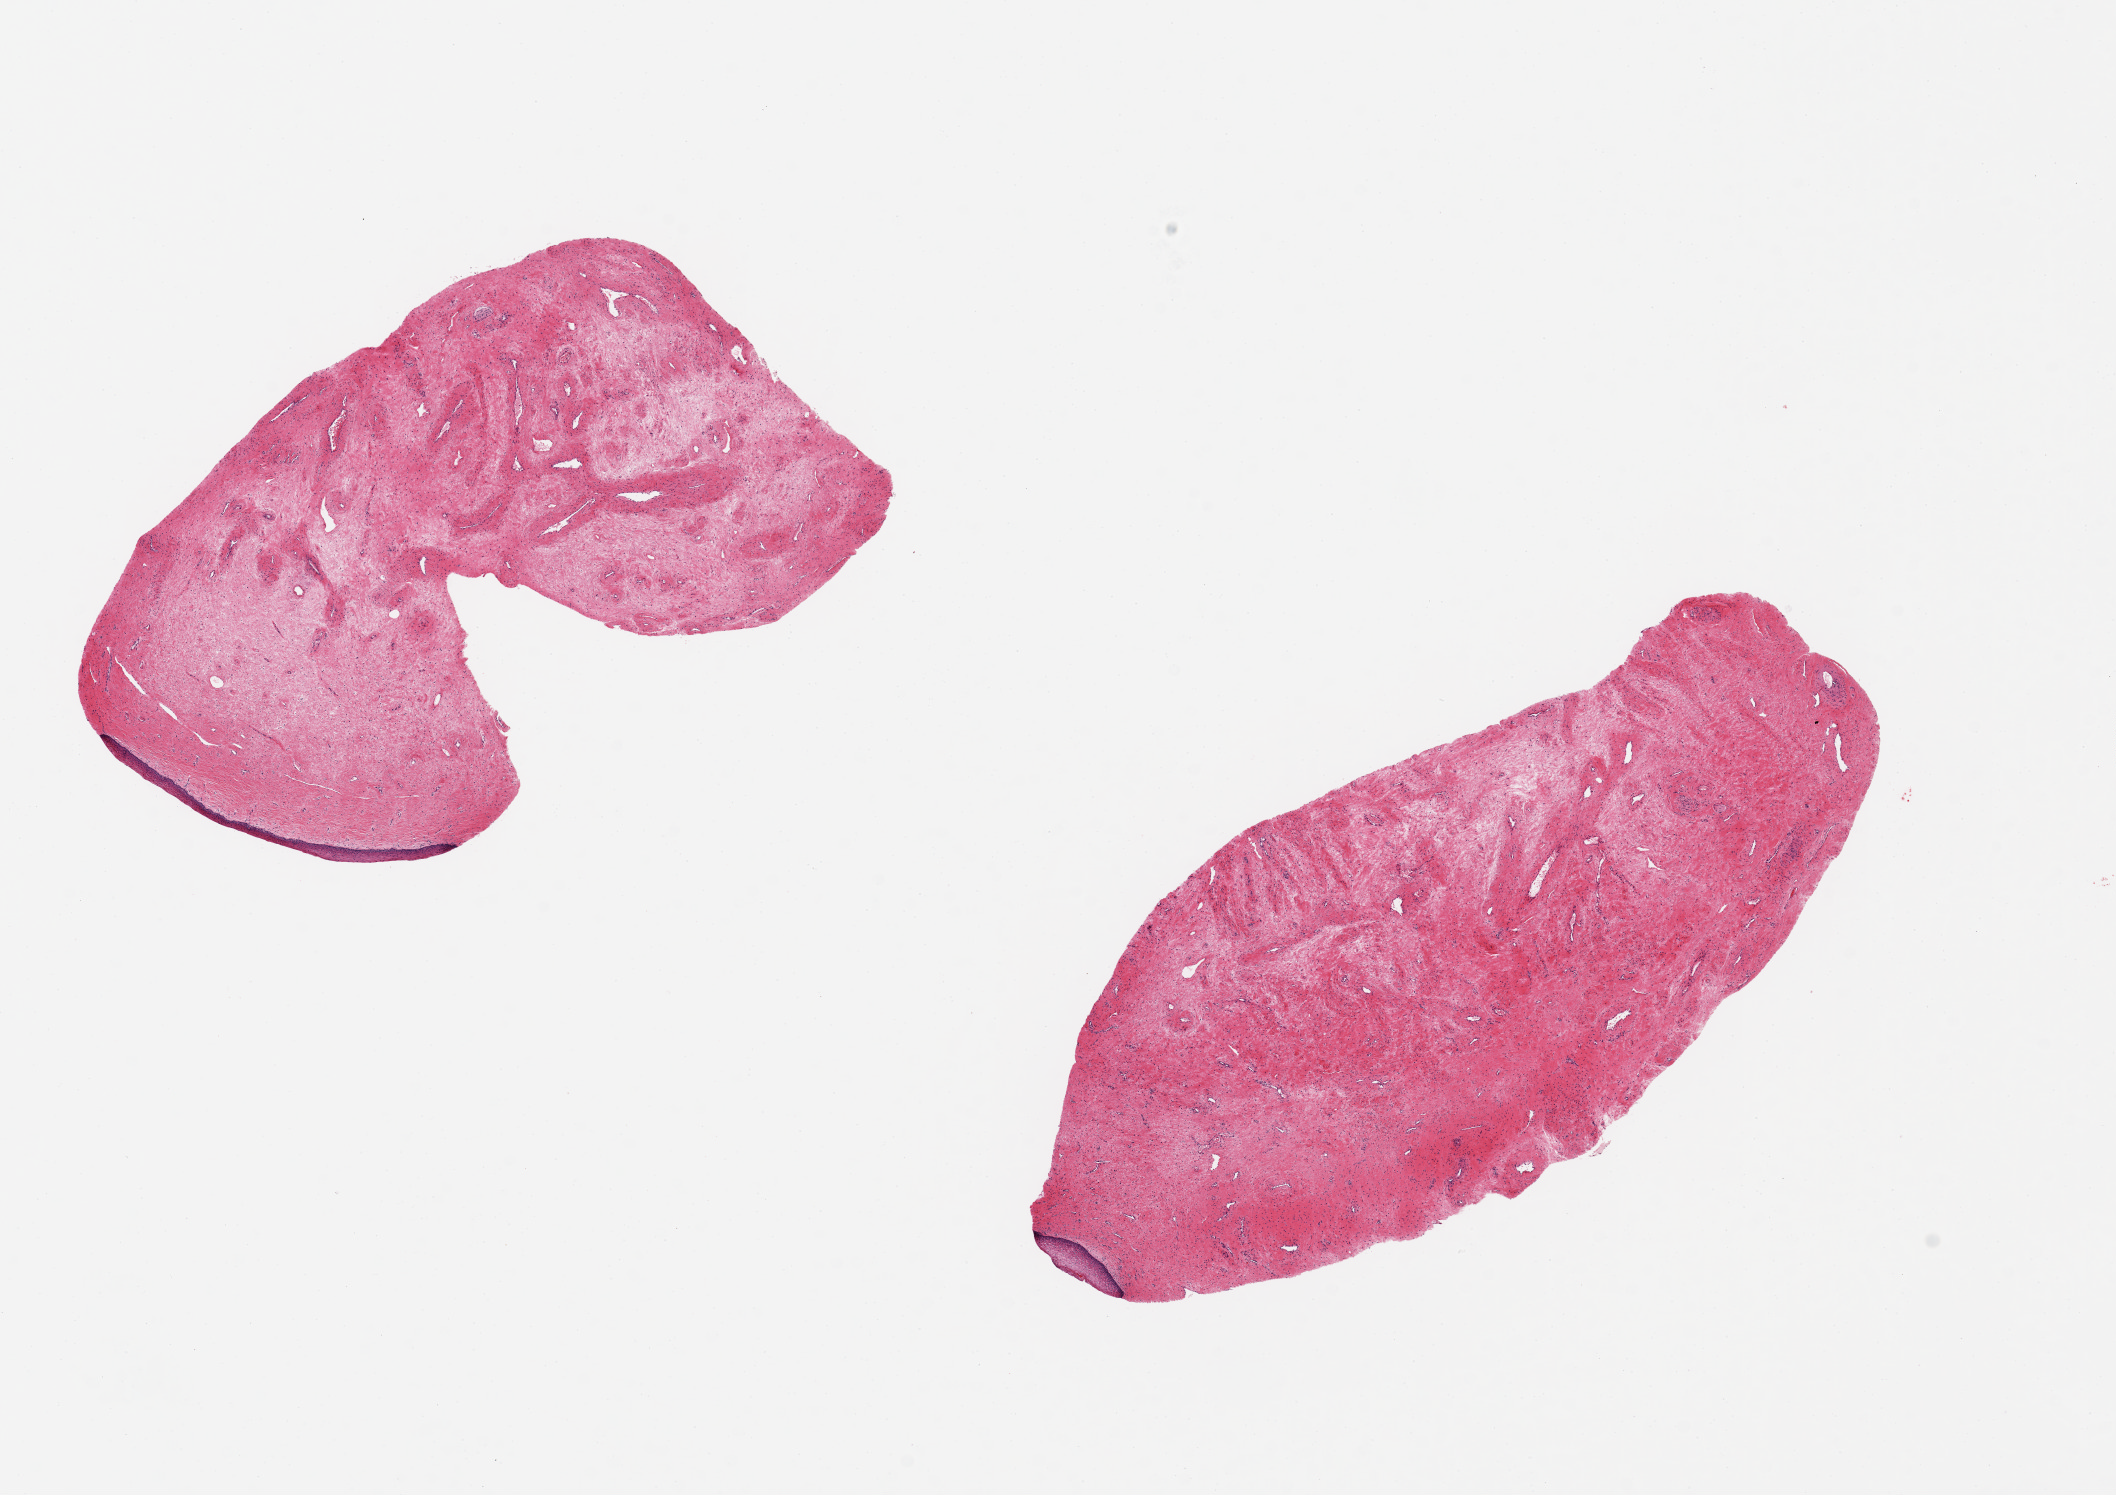
Whole-slide image, hematoxylin and eosin (H&E) stain, shown as a low-resolution overview of the whole scanned area (about 16.7 x 11.8 mm, from a 20x scan), PAXgene-fixed, paraffin-embedded tissue, section of exocervix (target tissue), tissue donor sample. Donor sex: female.
Reviewer comment on this tissue sample: 2 pieces 7x3 & 6x3 mm; limited mucosa on long piece.